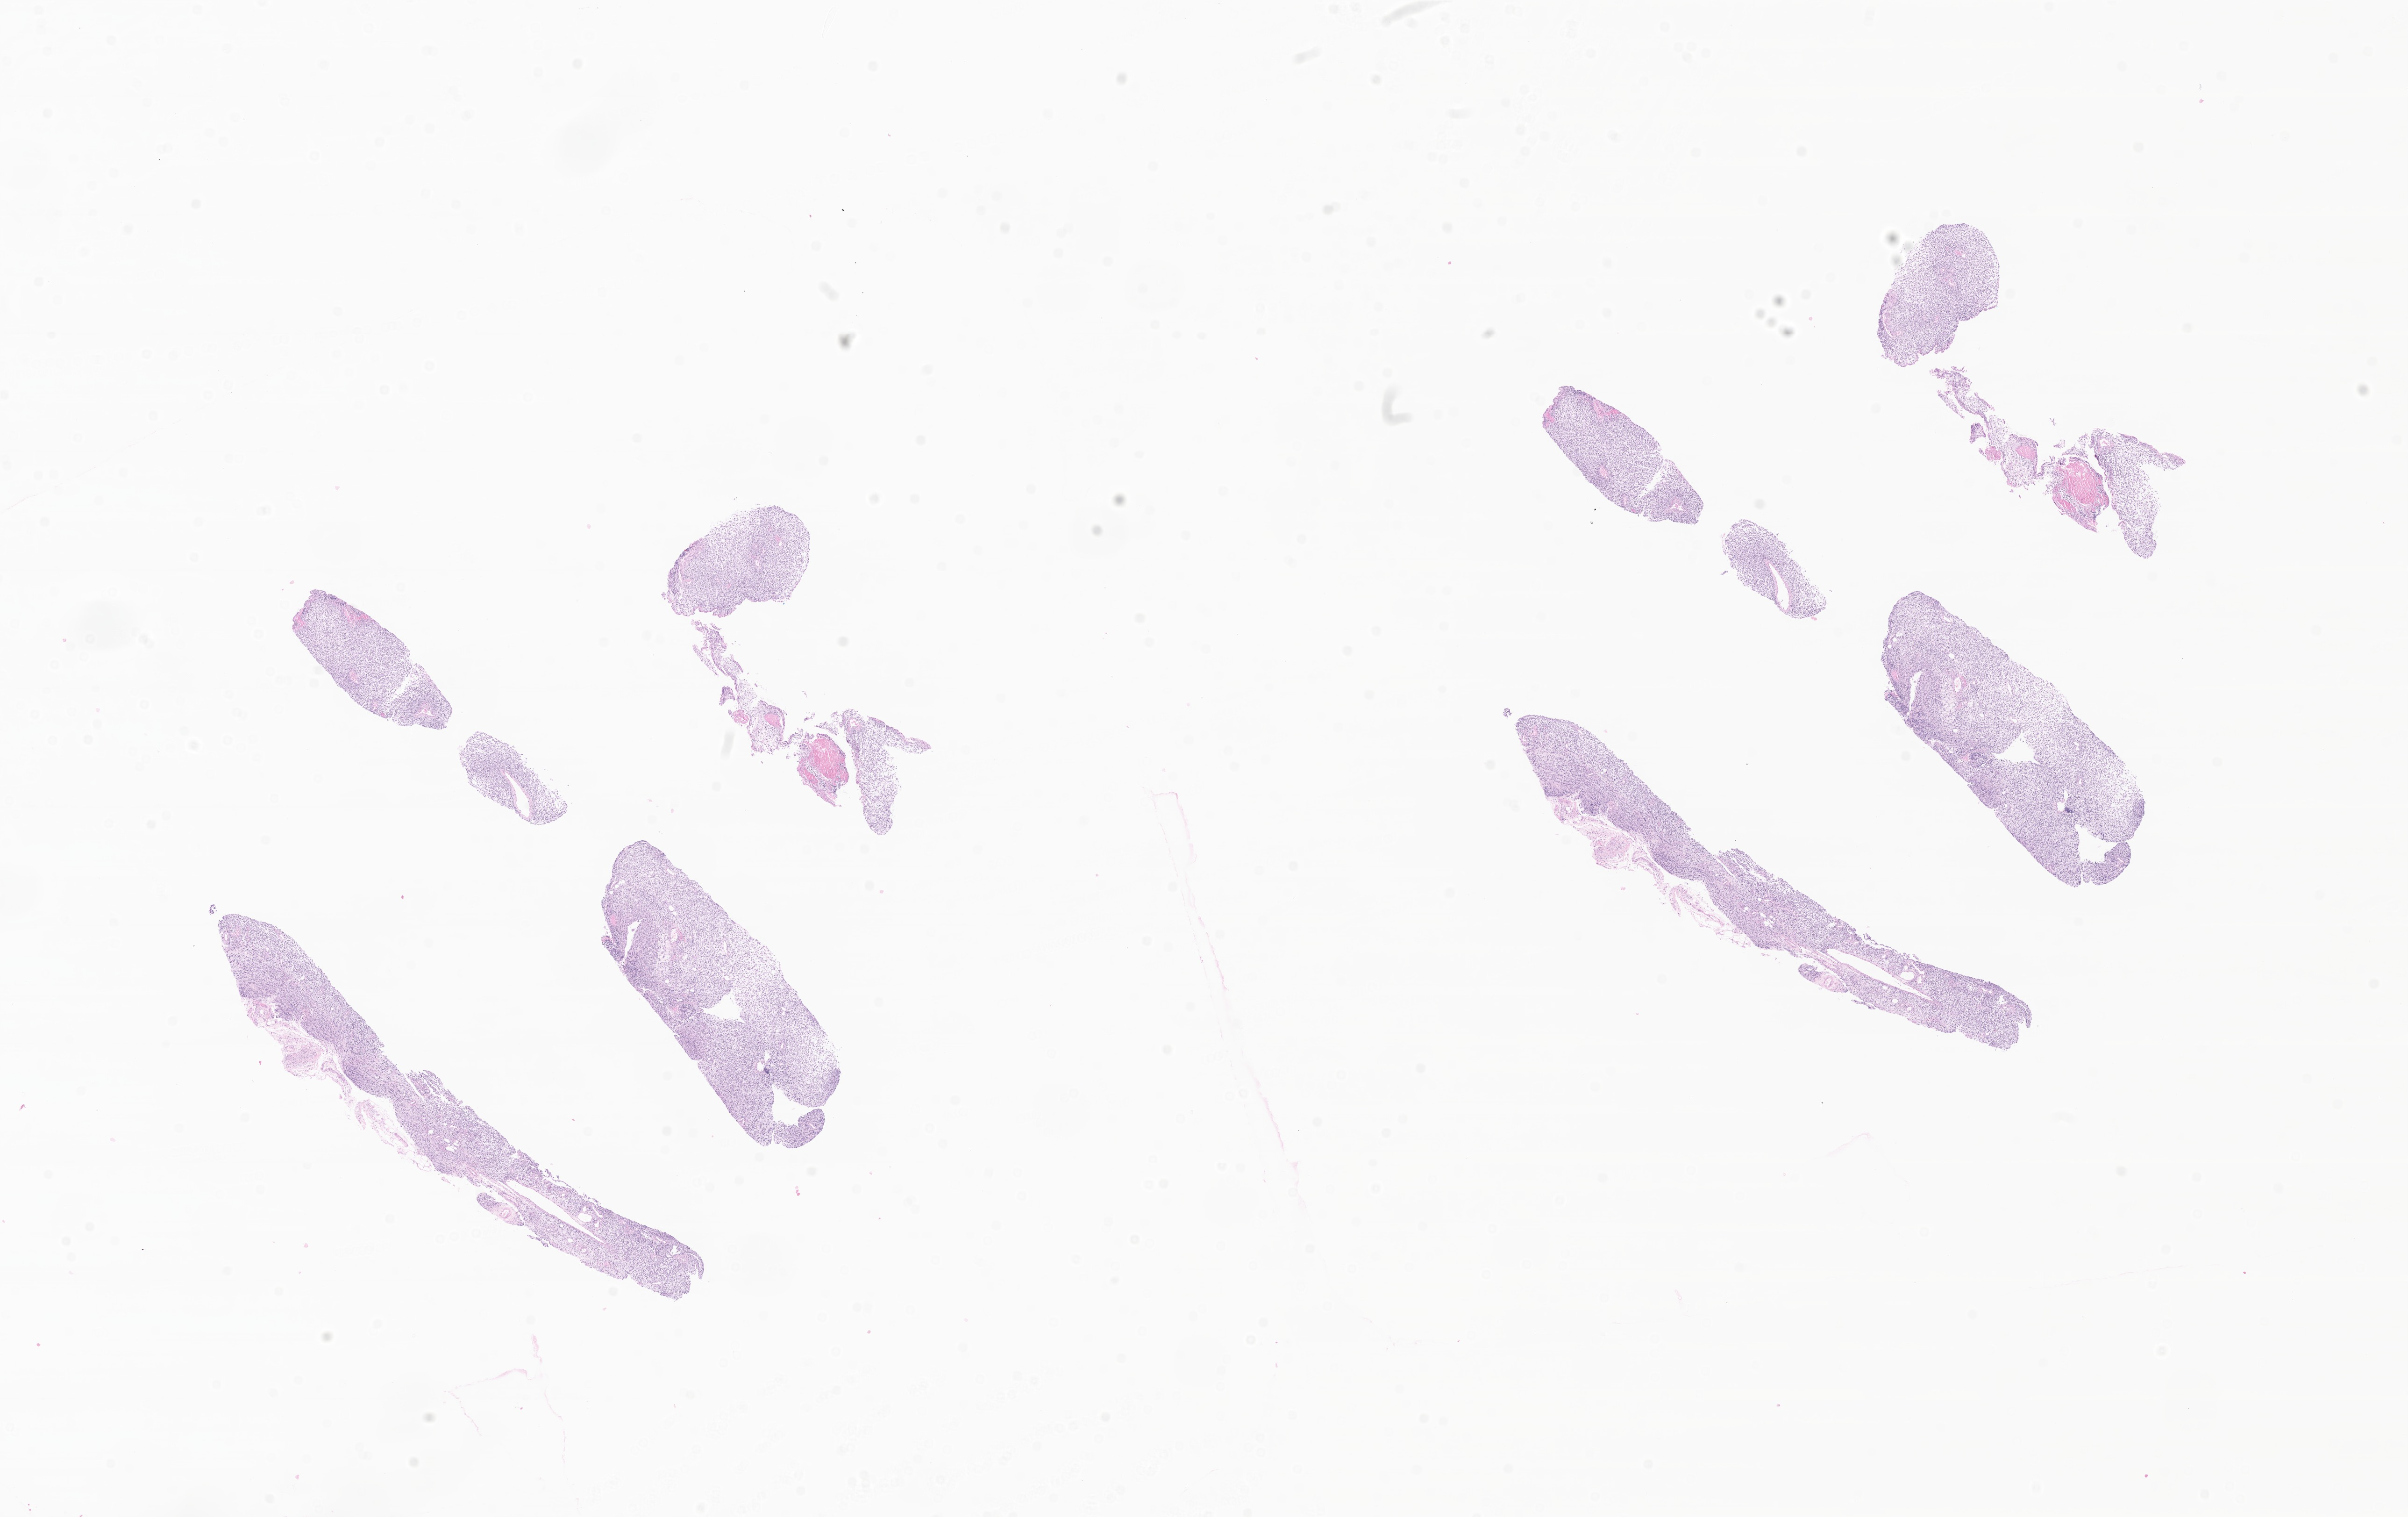
Haematoxylin and eosin whole-slide image of tumor tissue from the orbit — shown as a low-resolution overview of the whole scanned area (about 21.7 x 13.7 mm). Formalin-fixed paraffin-embedded section. Male patient, age 110 months (9 years 2 months).
Diagnosis: Embryonal rhabdomyosarcoma, NOS.